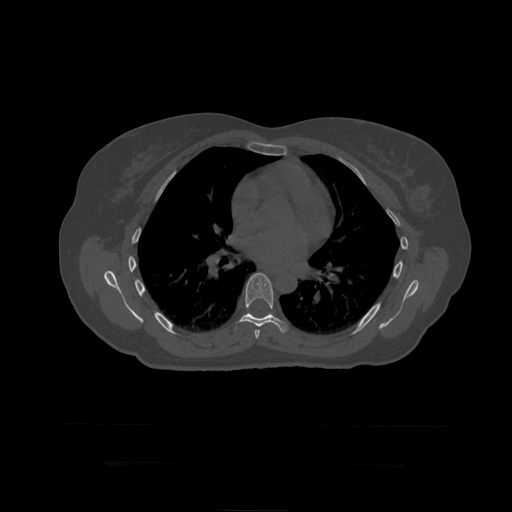
CT including the spine, one axial slice; slice 284 of 399 in the series (ordered by position); reconstruction kernel STANDARD; bone window (W 1800 / L 400 HU); 1.25 mm slice thickness; 512 × 512 image matrix, field of view 450 × 450 mm. Patient age 41 years. Case-level facts recorded for this patient, not image findings: primary cancer: breast.
Structures marked on this image (semi-automatic segmentation, software-assisted and operator-edited):
- T7 vertebra: bounding box (x1, y1, x2, y2) in pixels: (255, 330, 260, 339)
- T8 vertebra: (235, 273, 289, 334)